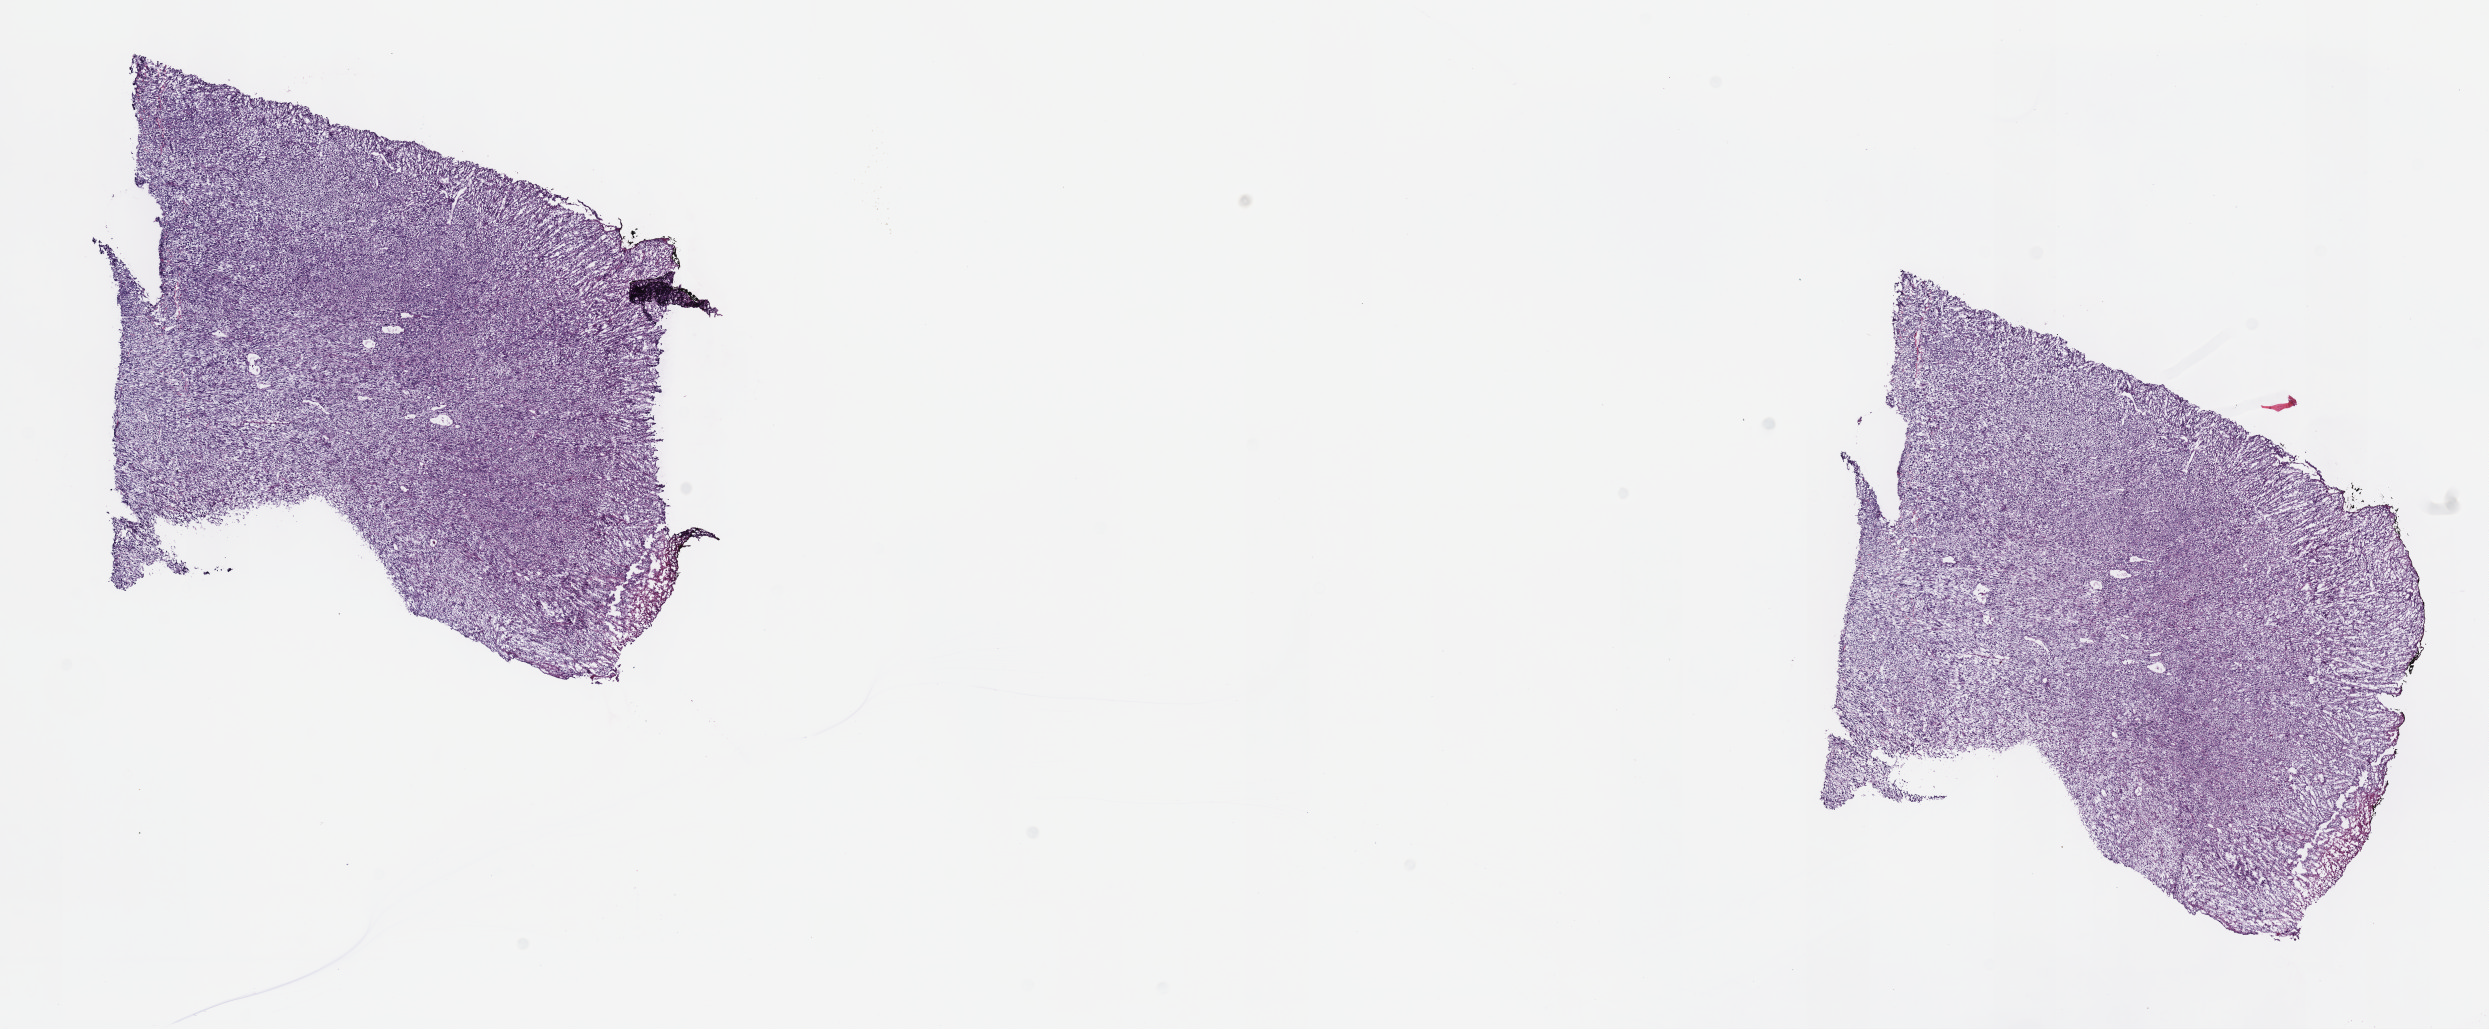
H&E-stained whole-slide image, a low-resolution overview of the entire scanned area, about 20.1 x 8.3 mm (acquisition: 40x scan); frozen section; retroperitoneum and peritoneum, primary tumour sample. Male patient; age at initial diagnosis 66 years. Pathologist review of this section (percent, as recorded): tumour cells 97%, tumour nuclei 80%, normal cells 0%, stromal cells 0%, necrosis 3%. Infiltration values recorded for this section: lymphocyte infiltration 1%, monocyte infiltration 0%, neutrophil infiltration 0%.
Histologic diagnosis: Dedifferentiated liposarcoma.